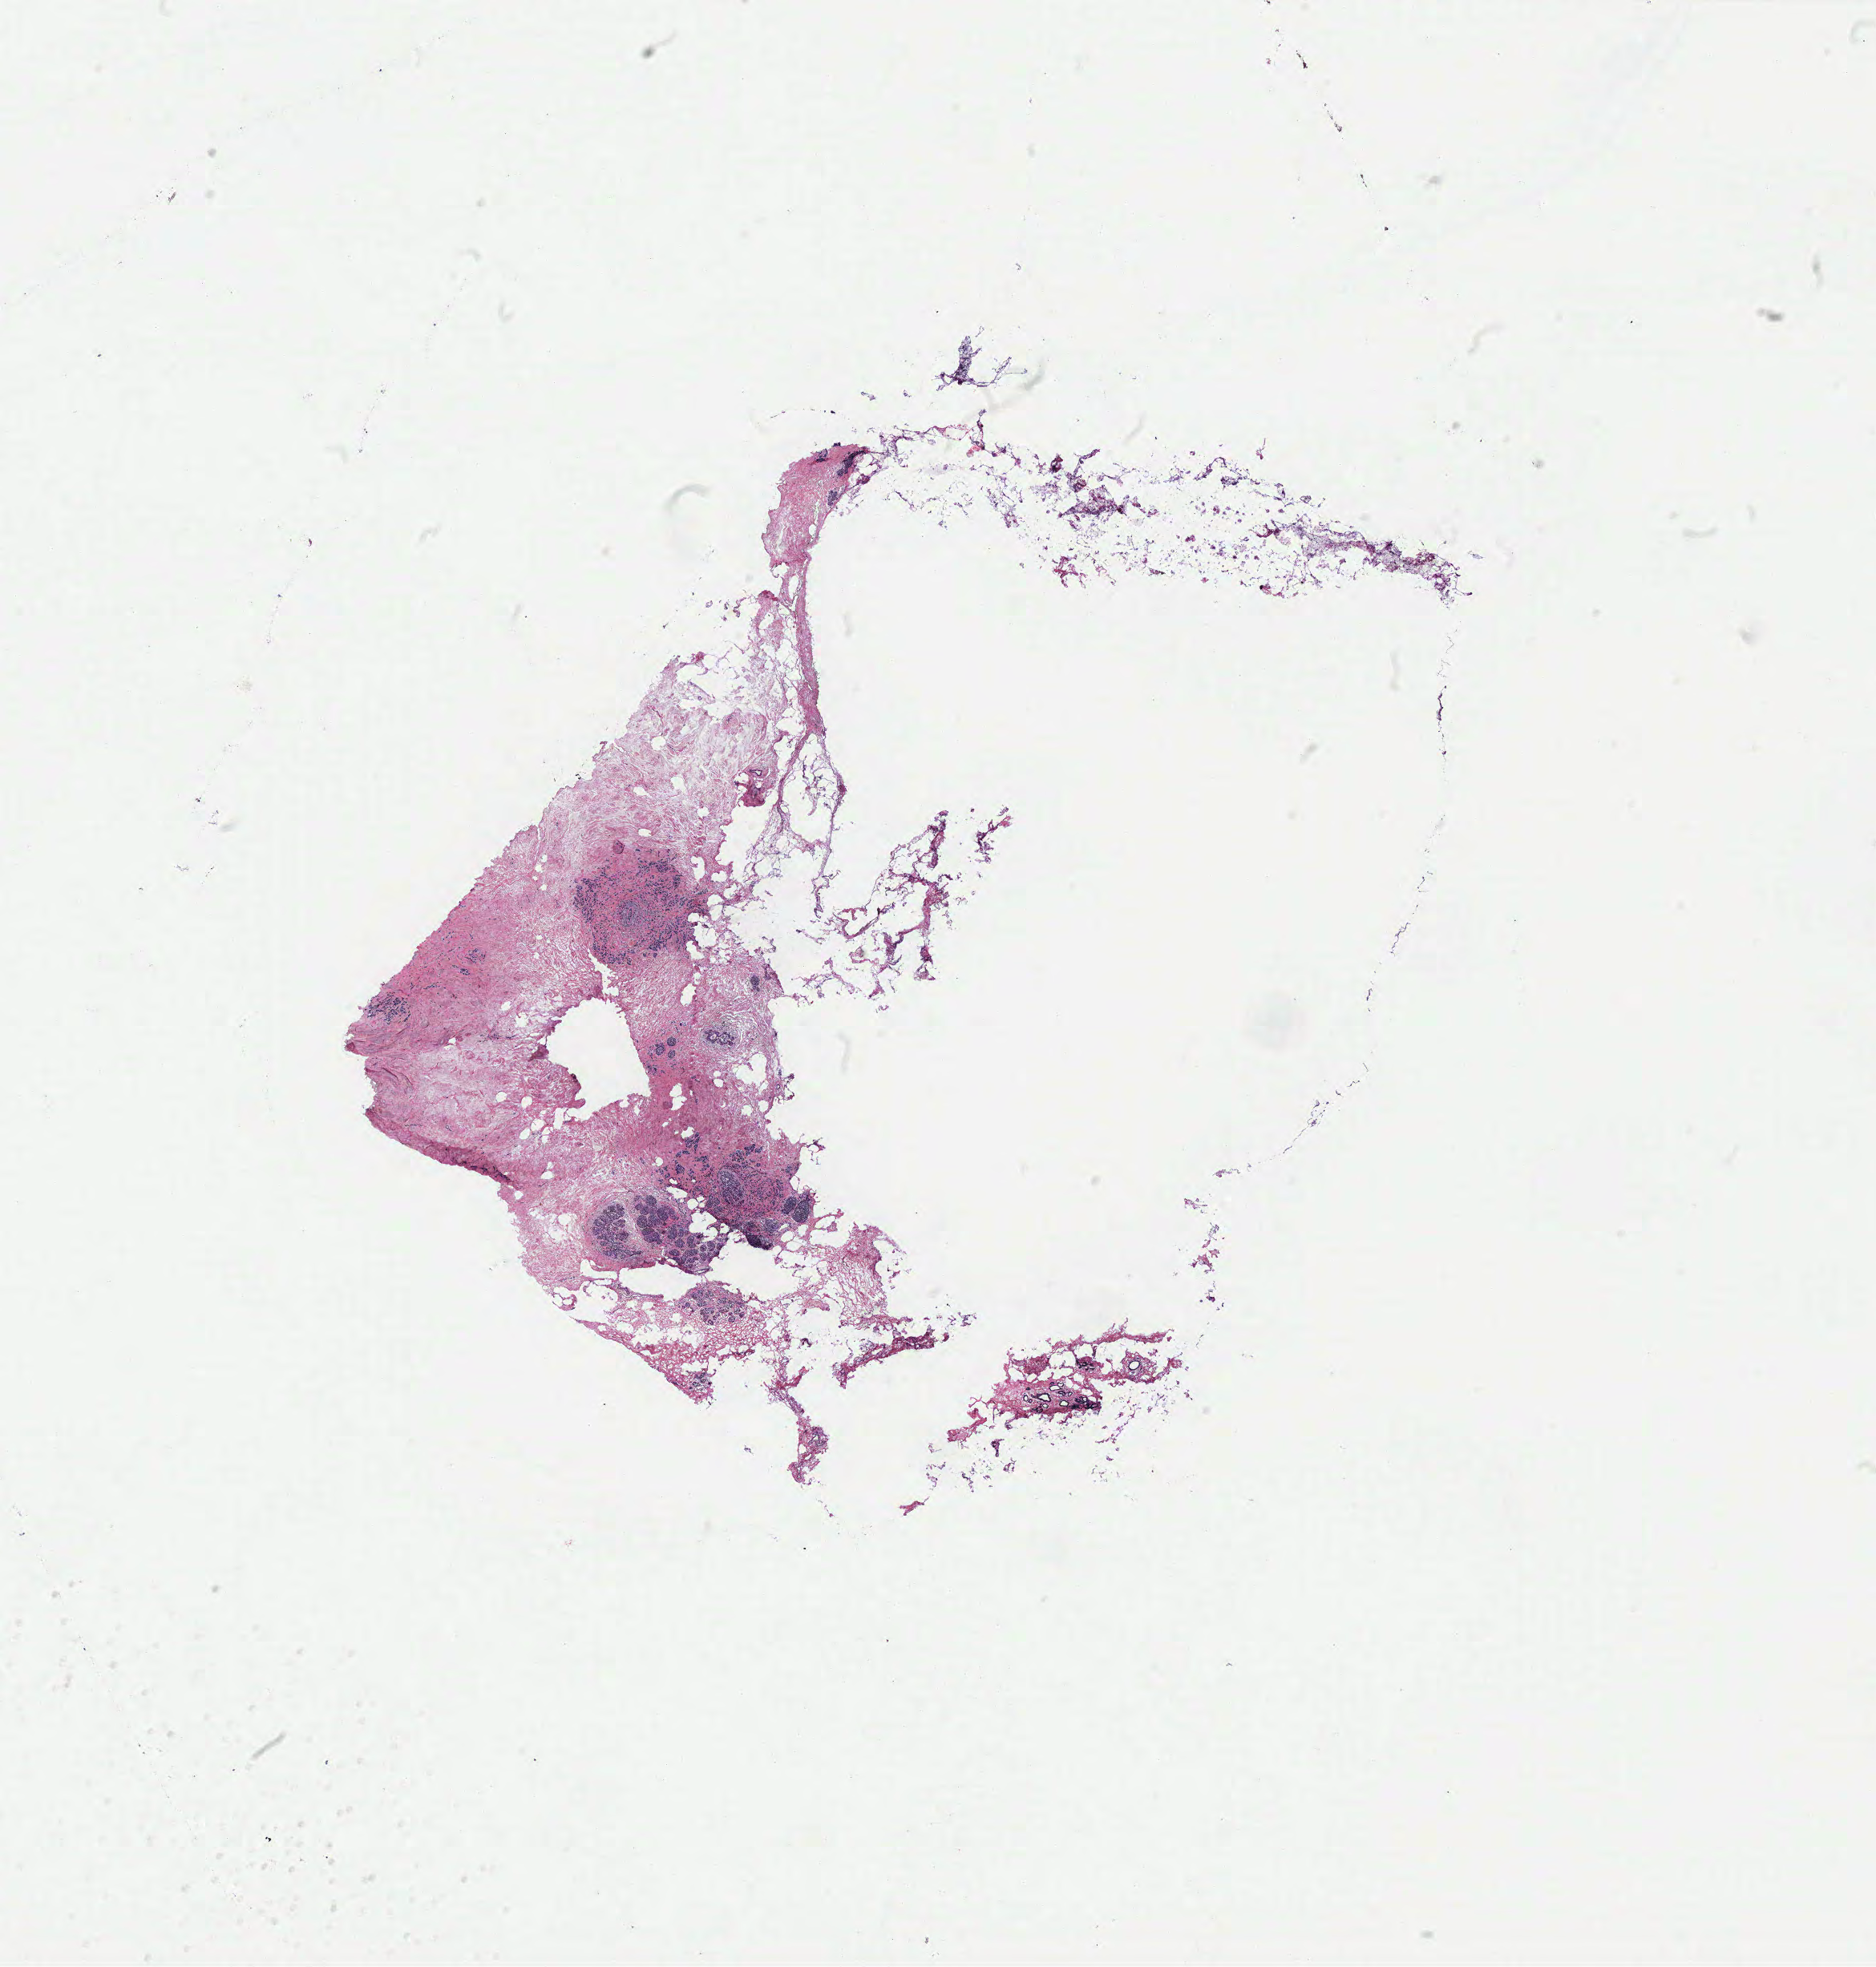
Hematoxylin and eosin (H&E) stained whole-slide image, shown as a low-resolution overview of the whole scanned area (about 18.7 x 19.6 mm, slide scanned at 40x); breast, tumour tissue. Patient: female, age 66 years.
AJCC pathologic stage: IIIA. Diagnosis: Infiltrating lobular carcinoma, NOS.